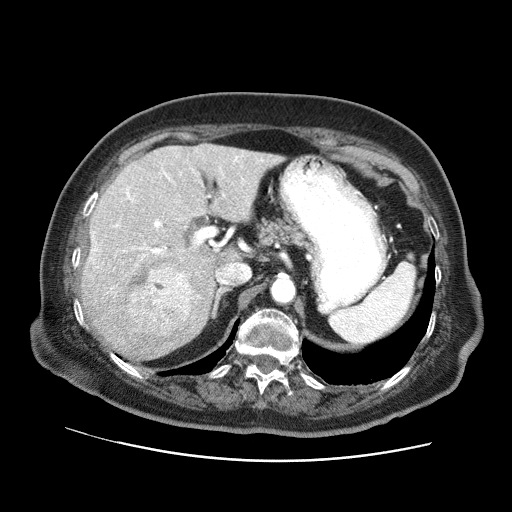
Contrast-enhanced abdominal CT (liver protocol), one axial slice; slice 43 of 73 in the series (ordered by position); reconstruction kernel STANDARD; soft-tissue window (W 400 / L 40 HU); 2.5 mm slice thickness; 512 × 512 image matrix. From the clinical record (not read from this slice): diagnosis: hepatocellular carcinoma (patient treated with transarterial chemoembolisation; whether this scan precedes or follows treatment is not stated here); TNM stage (as recorded): Stage-I; Child-Pugh class: A; tumour nodularity: uninodular.
Outlined on this slice (semi-automatically segmented with operator editing):
- liver parenchyma outside the tumour (the mass and vessels are separate outlines, so this box may not span the whole liver): bounding box (x1, y1, x2, y2) in pixels: (82, 144, 282, 360)
- mass: (125, 264, 199, 337)
- liver vessels: (91, 155, 262, 259)